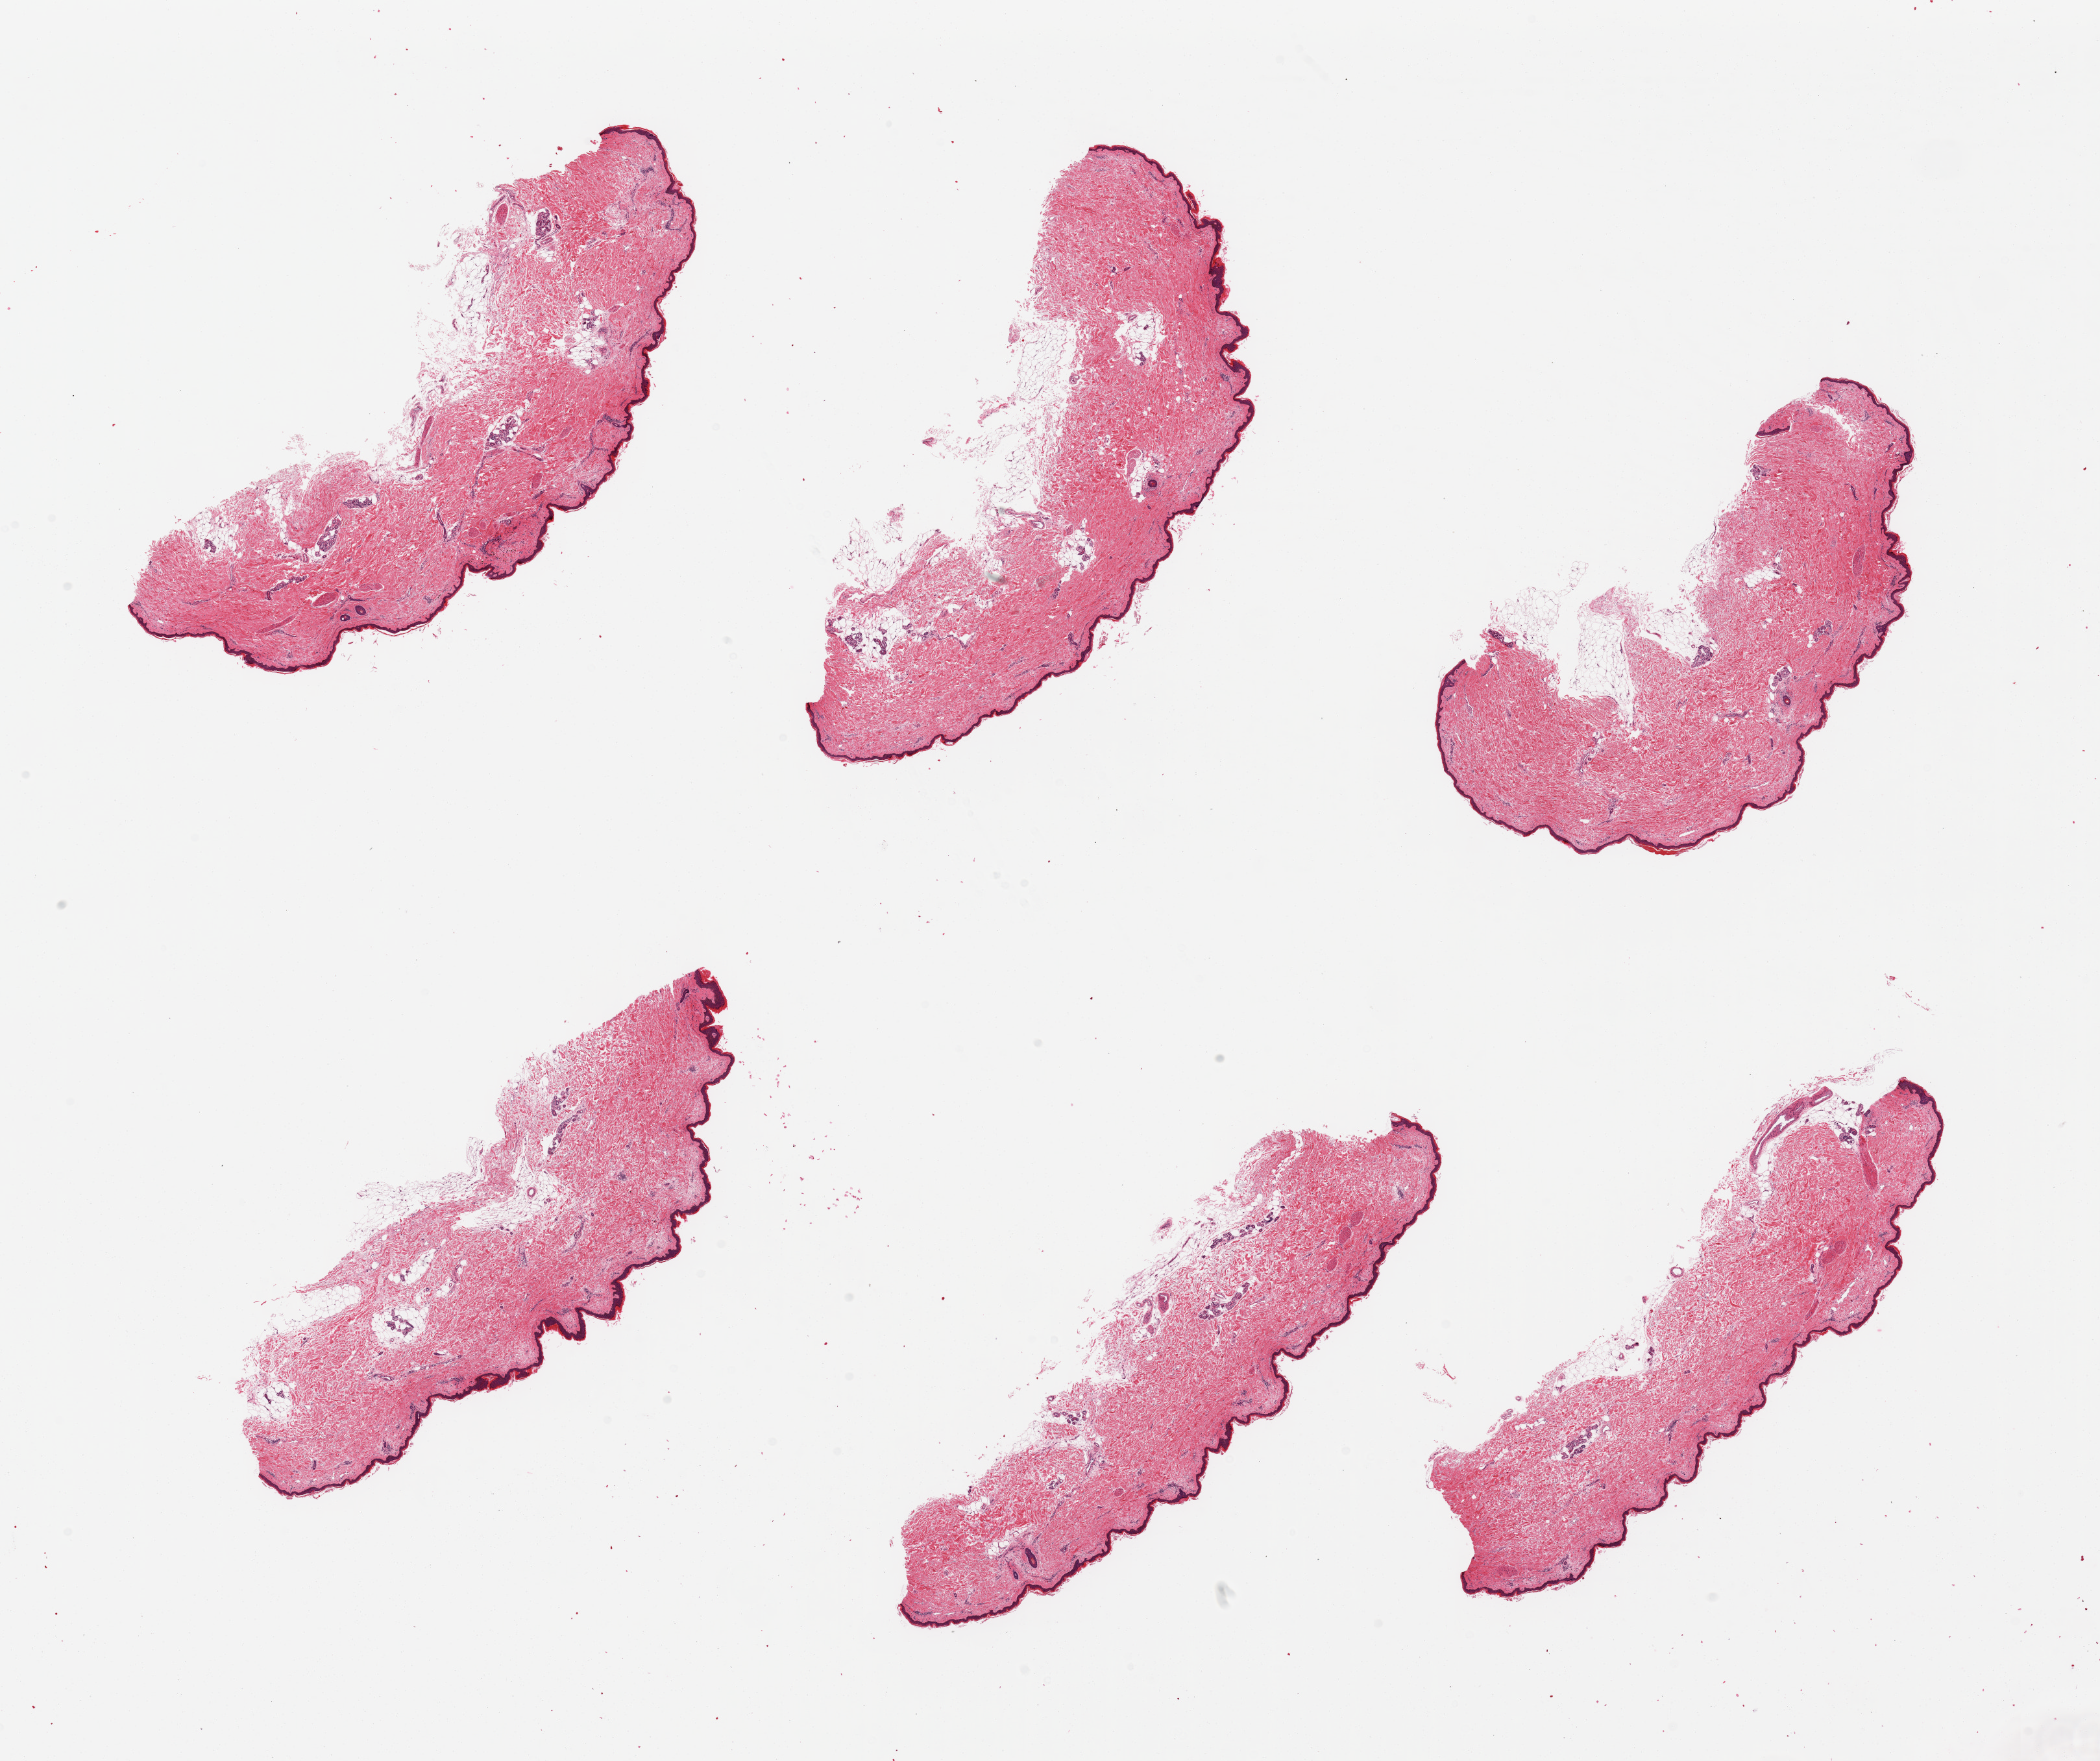
Whole-slide image, haematoxylin and eosin stain — shown as a low-resolution overview of the whole scanned area (about 25.6 x 21.5 mm), PAXgene-fixed, paraffin-embedded tissue, sampled site (target tissue): skin of lower leg, donor tissue sample. Donor sex: female.
Pathologist's review note for this sample: 6 pieces, minimal dermal fat; squamous epithelium is ~50microns.